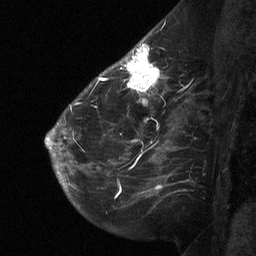
Breast MRI (dynamic contrast-enhanced), one sagittal slice. Slice 41 of 64 in the series (ordered by position). Dynamic contrast-enhanced study with each time point stored as its own series, time point 2 of 3 at this slice position (early post-contrast, ordered by acquisition time). 1.5 T. TE 4.8 ms, TR 27 ms. 2 mm slice thickness. 256 × 256 image matrix, field of view 200 × 200 mm. Female patient, age 51 years. From the clinical record (not read from this slice): setting: breast cancer imaged before/during neoadjuvant chemotherapy; receptor status: HR-positive, HER2-negative.
Structures marked on this image (semi-automatic segmentation, software-assisted and operator-edited):
- analysis volume of interest (the breast-tissue region the enhancement analysis was run in; not a lesion): bounding box (x1, y1, x2, y2) in pixels: (112, 46, 169, 106)
- tumour enhancement mask (voxels above the 90 % enhancement threshold inside the analysis volume of interest): (123, 46, 160, 103)